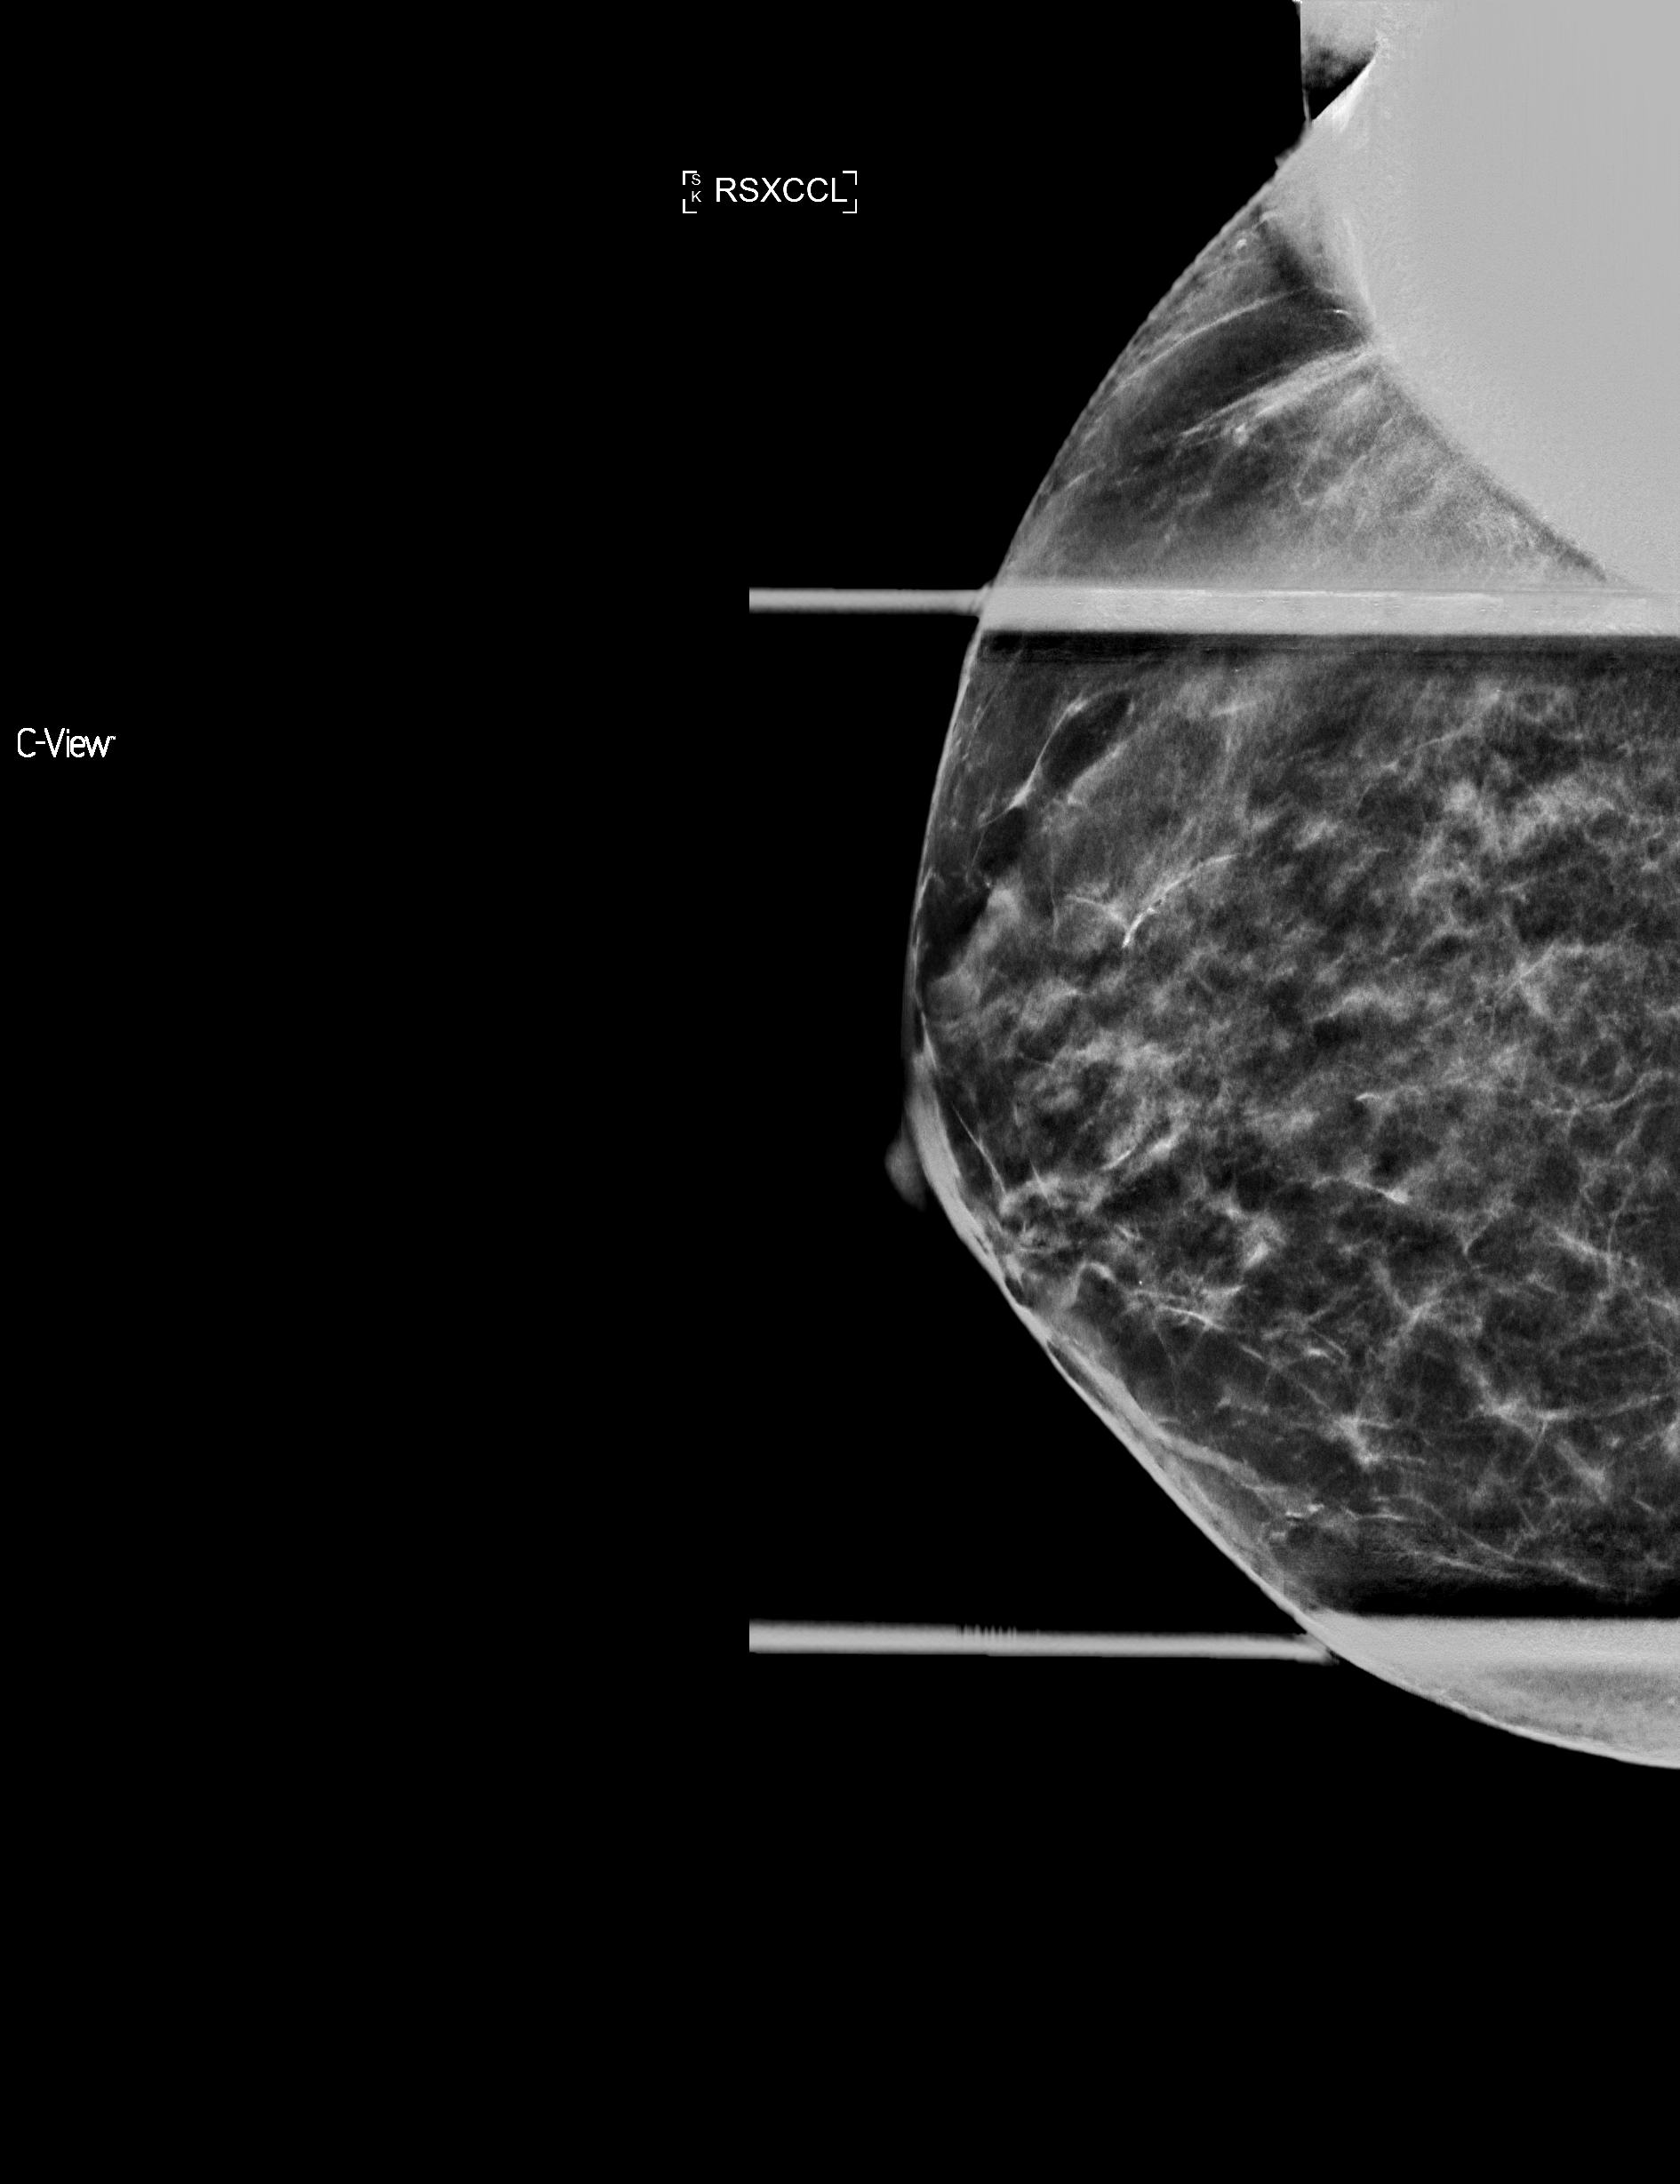
Full-field digital mammogram (FFDM), right breast, laterally exaggerated craniocaudal (XCCL) view (spot compression), annual screening mammography examination, system: Selenia Dimensions. Female patient, age 59 years.
BI-RADS breast density category at the screening exam (both breasts, scale 1–4): 3. Final BI-RADS category for the screening round (tomosynthesis exam, both breasts): category 1. Recall: no recall after this screen.